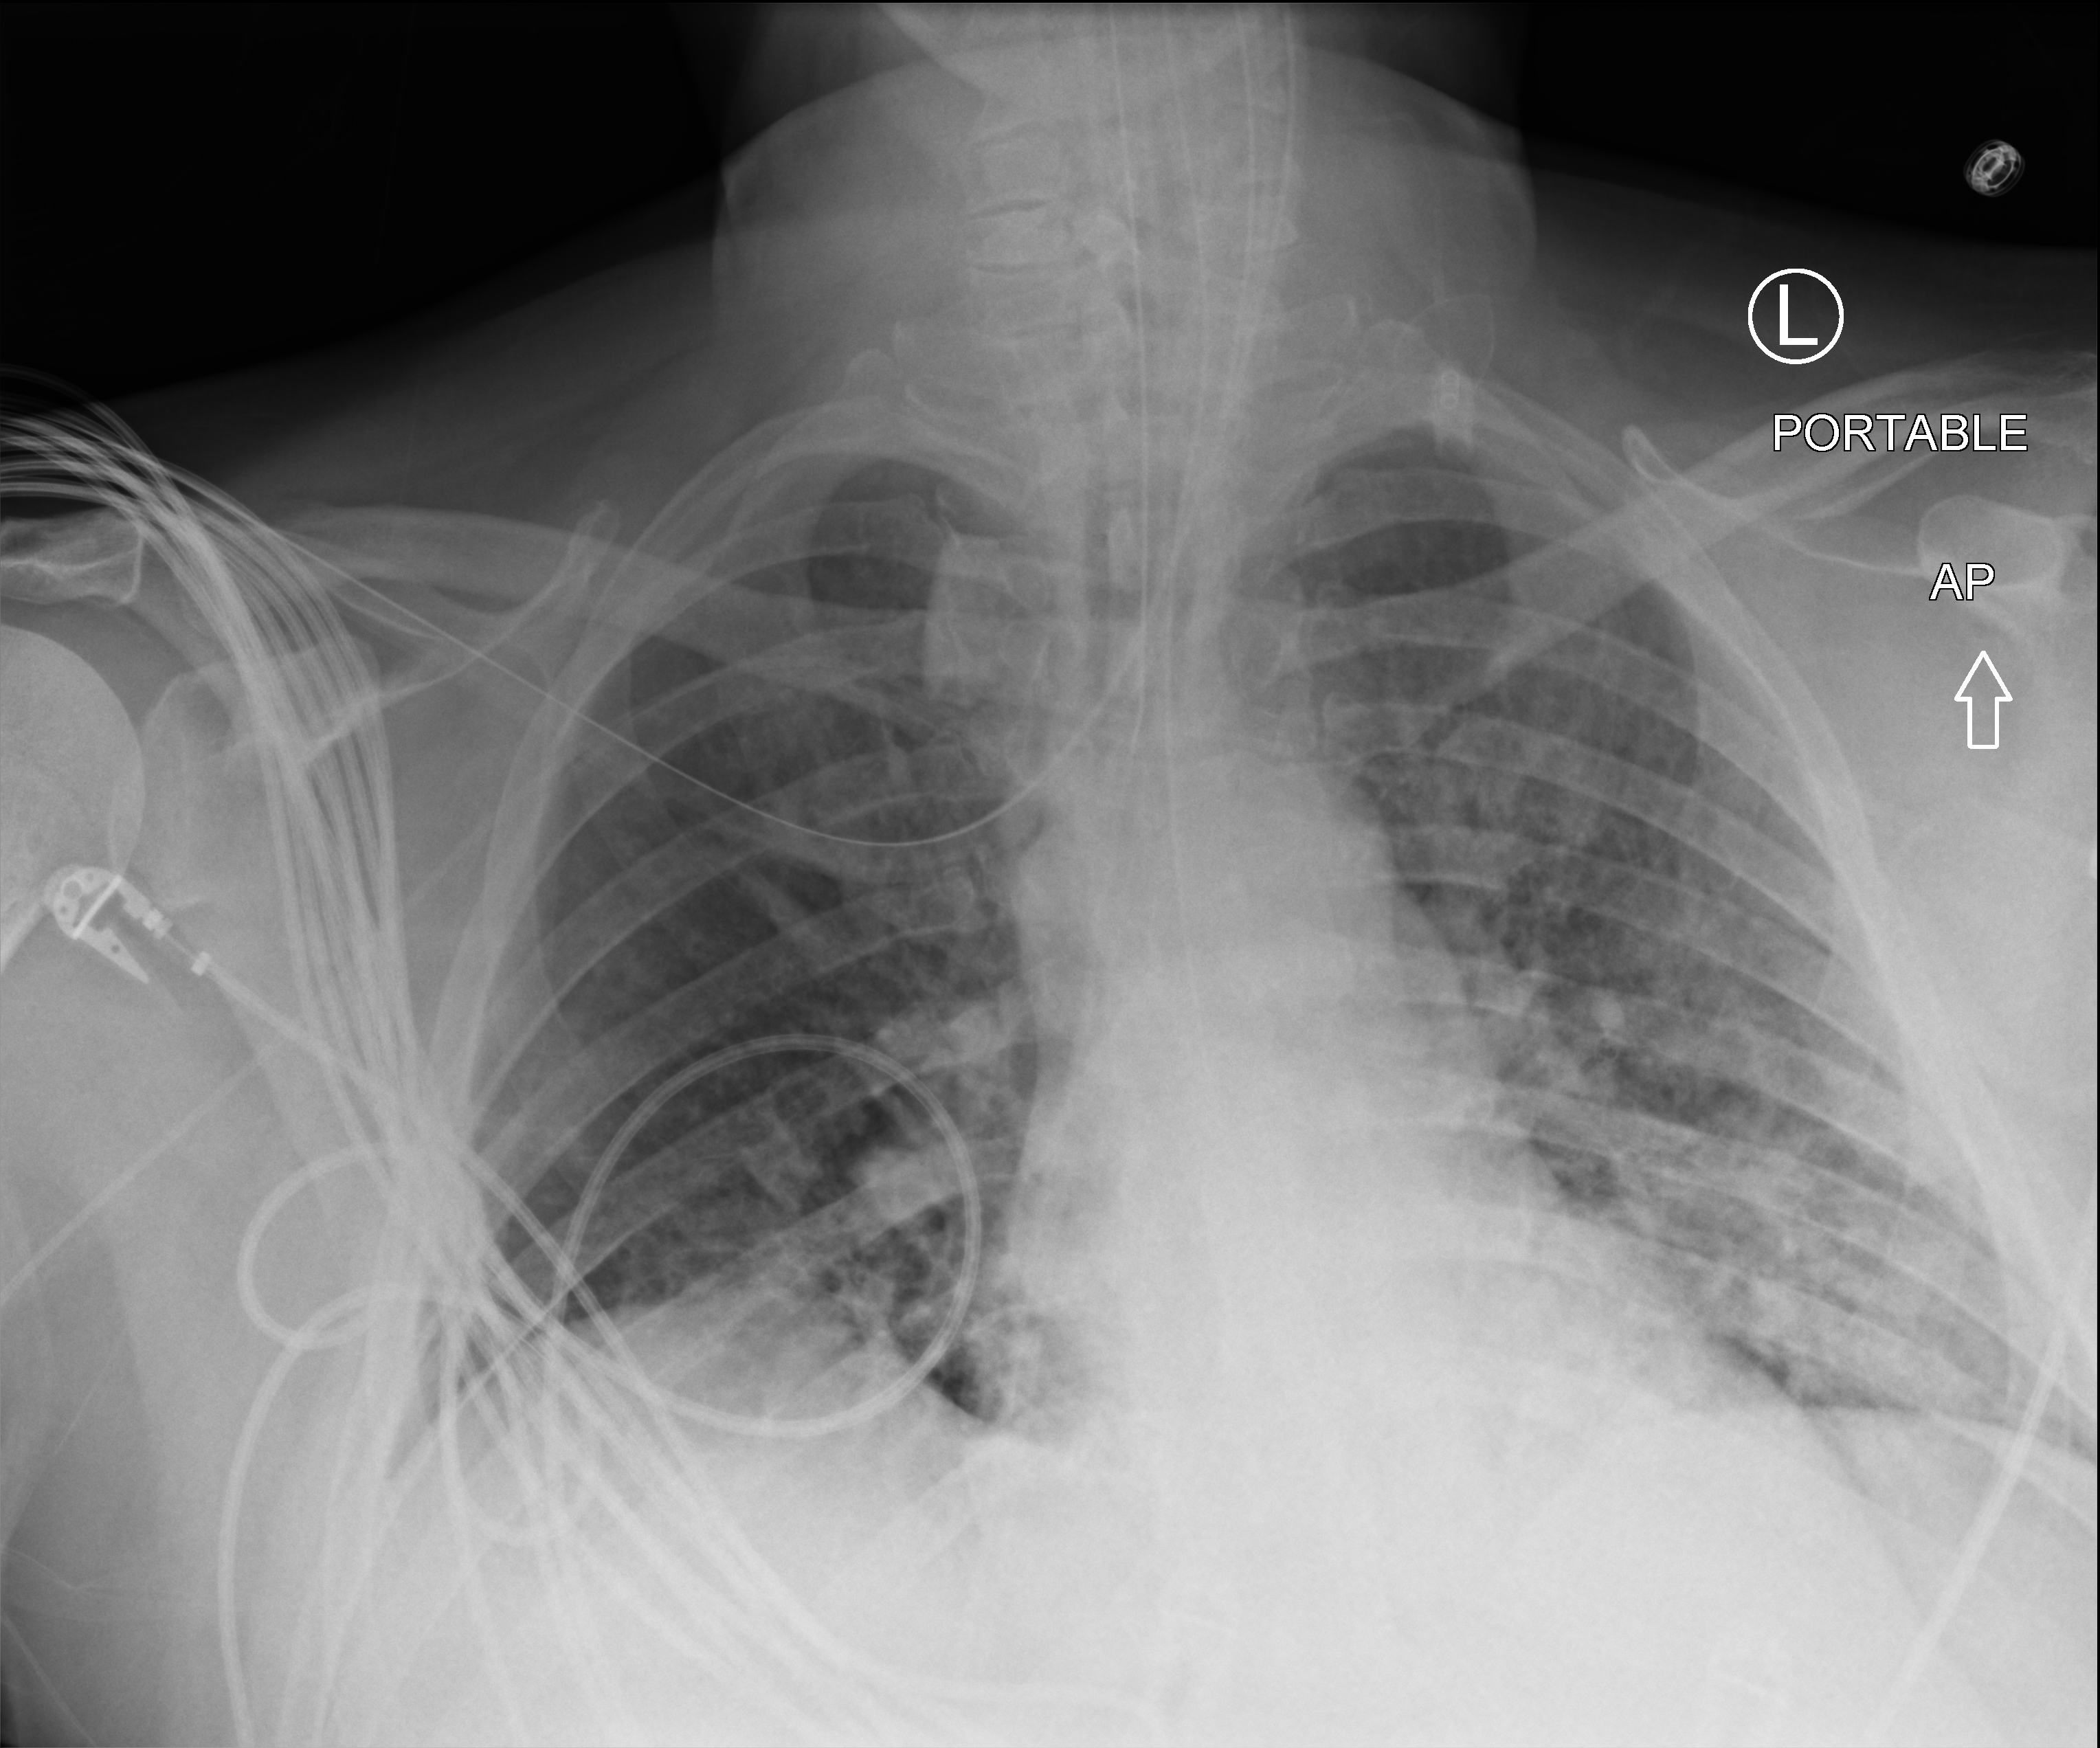
Bedside chest radiograph (computed radiography), anteroposterior (AP) projection. Patient hospitalised with COVID-19; male, aged 18–59 years.
From the hospital-stay record, not from the radiograph (when in the stay this image was taken is not recorded): admitted to intensive care during this hospital stay: yes; mechanically ventilated during this hospital stay: yes; diabetes (admission record): yes.